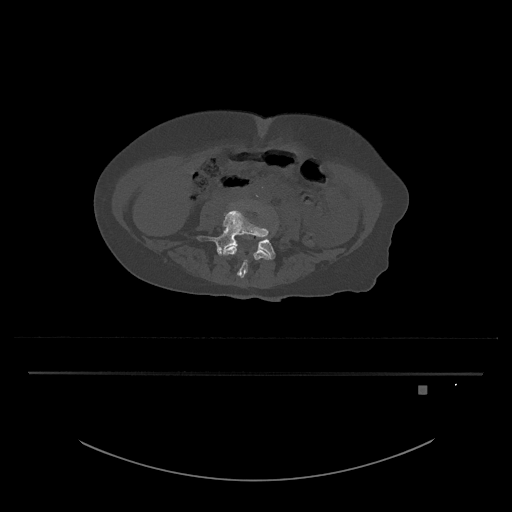
CT including the spine, one axial slice; position 329 of 797 along the scan axis; bone window (W 1800 / L 400 HU); 0.5 mm slice thickness; 512 × 512 image matrix. Female patient, age 57 years. From the clinical record (not read from this slice): primary cancer: cervical.
Structures marked on this image (semi-automatic segmentation, software-assisted and operator-edited):
- L4 vertebra: bounding box (x1, y1, x2, y2) in pixels: (222, 245, 271, 278)